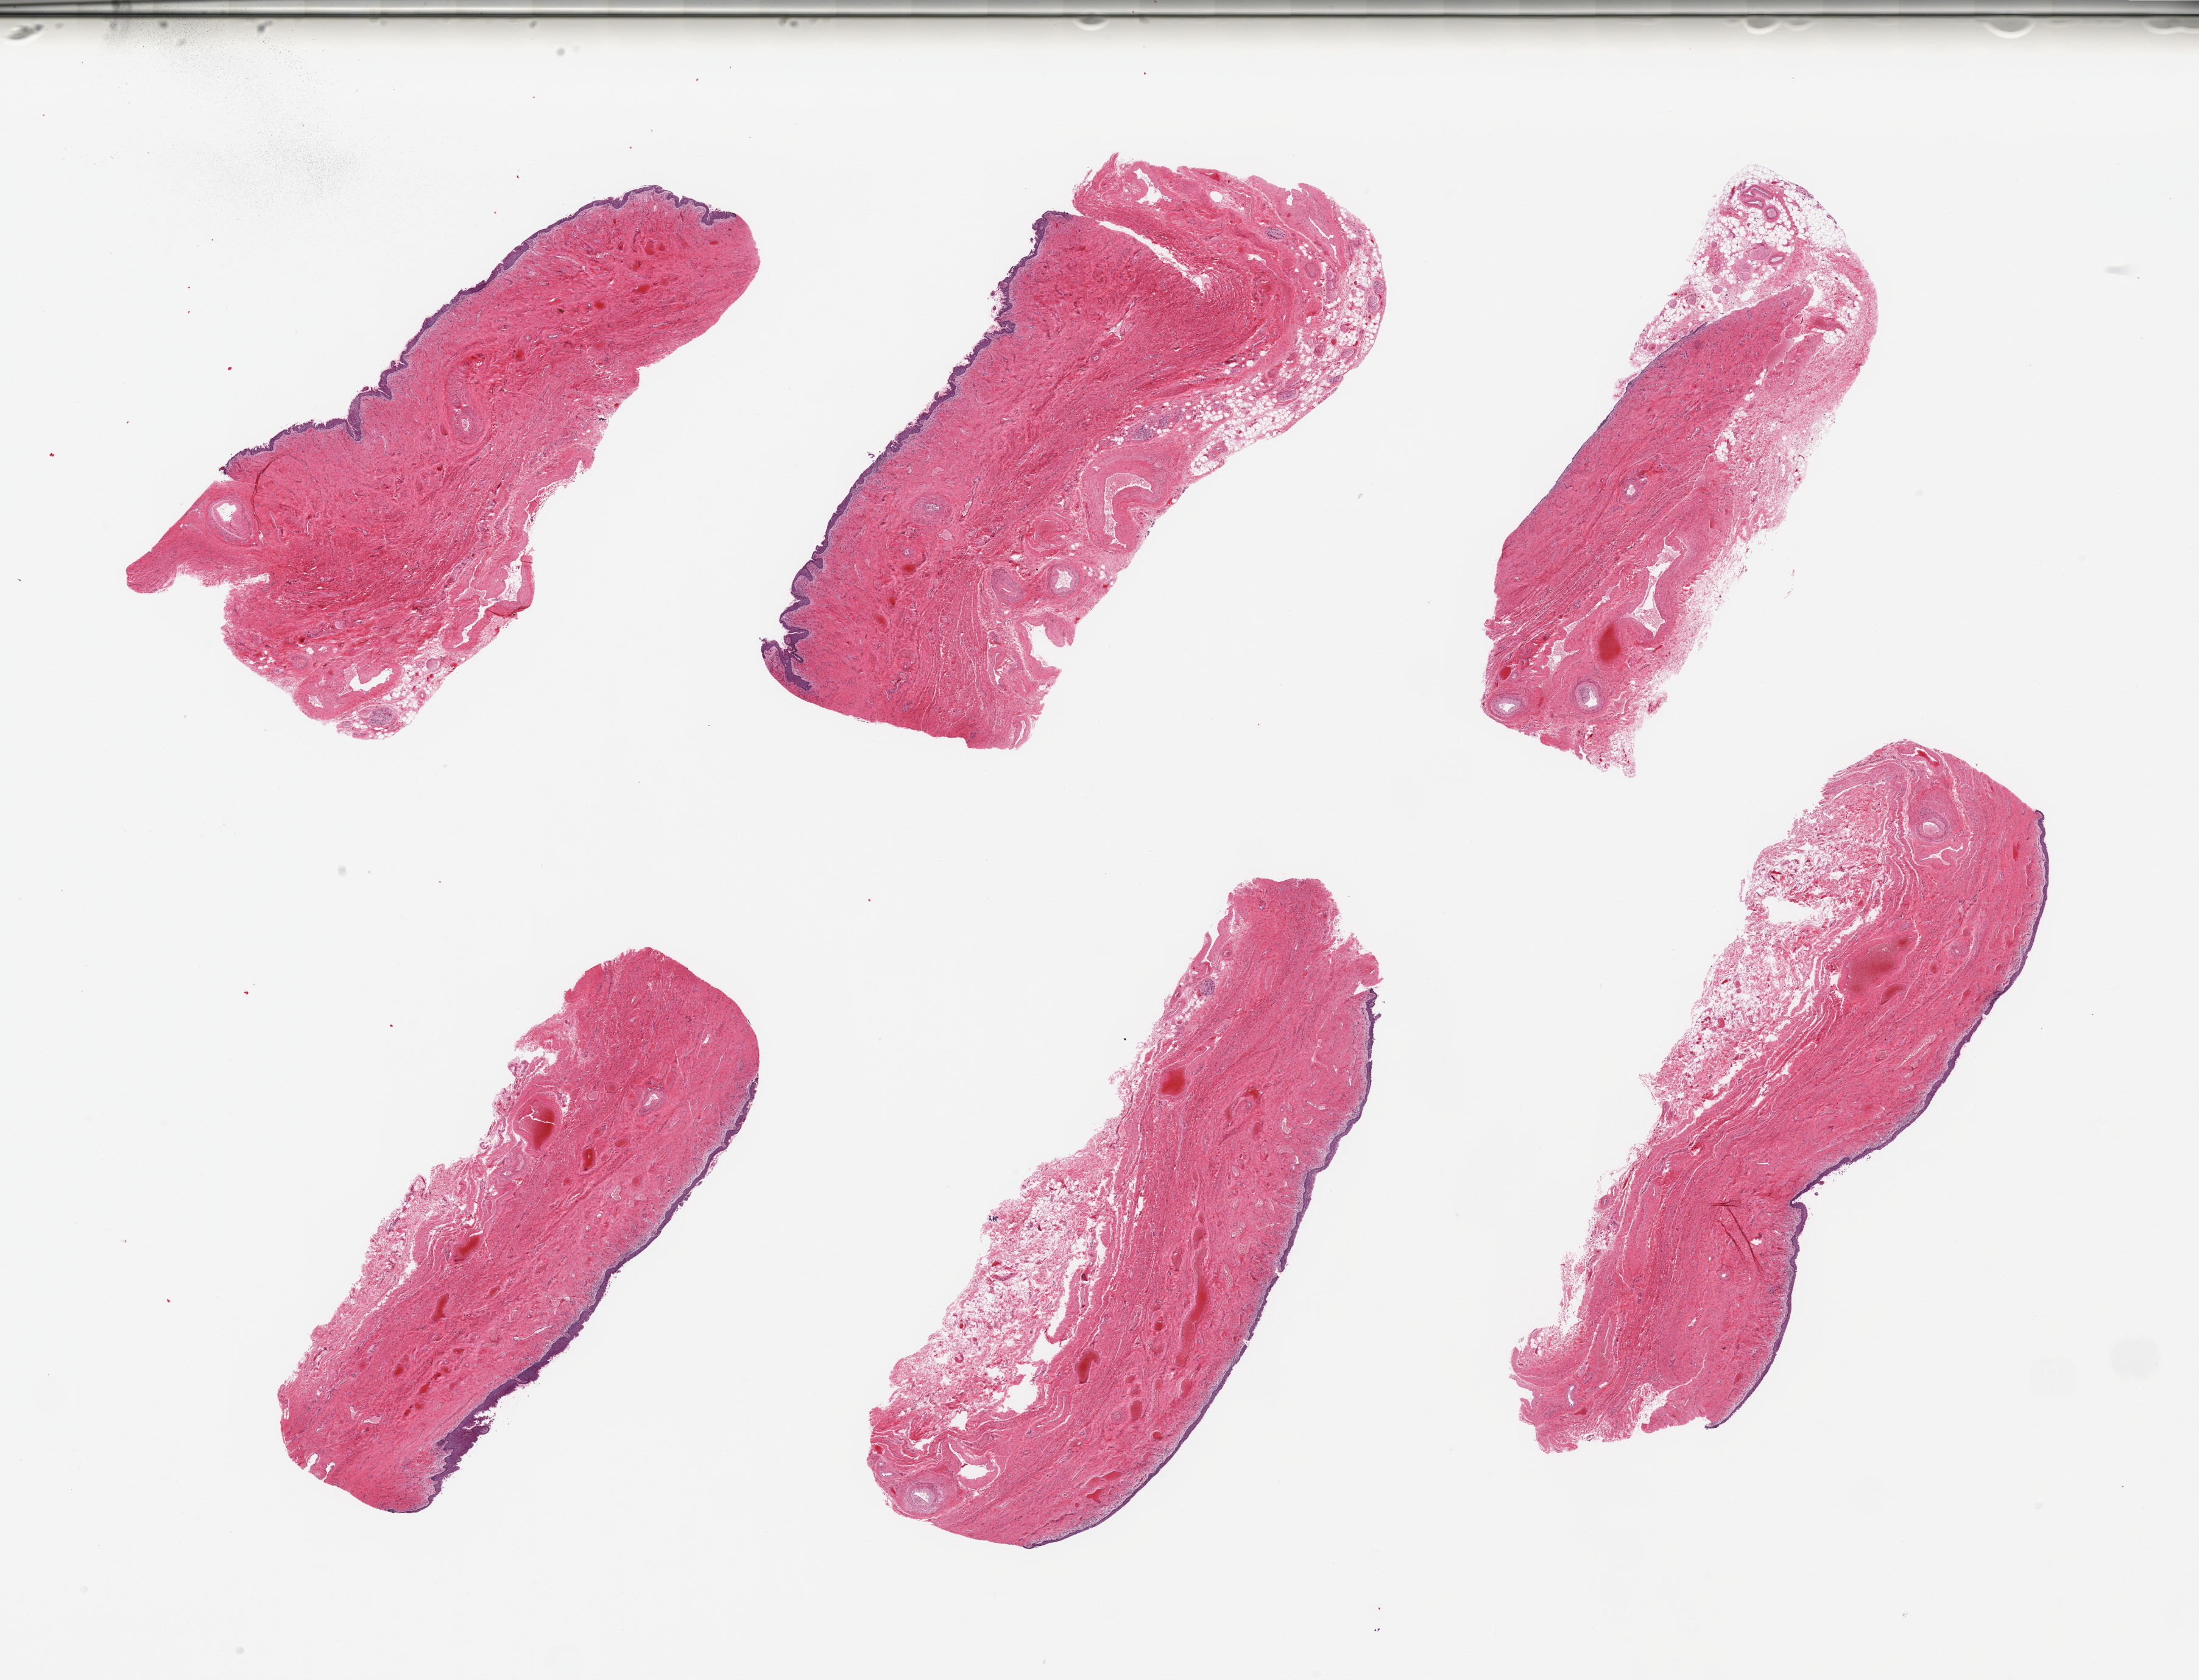
Digitized haematoxylin and eosin-stained section, shown as a low-resolution overview of the whole scanned area (about 28.5 x 21.8 mm); PAXgene-fixed paraffin-embedded (PFPE) section; target tissue: vagina; tissue donor sample. Donor: female.
Pathologist's review note for this sample: 6 pieces, squamous mucosa sloughing, up to ~70 microns.